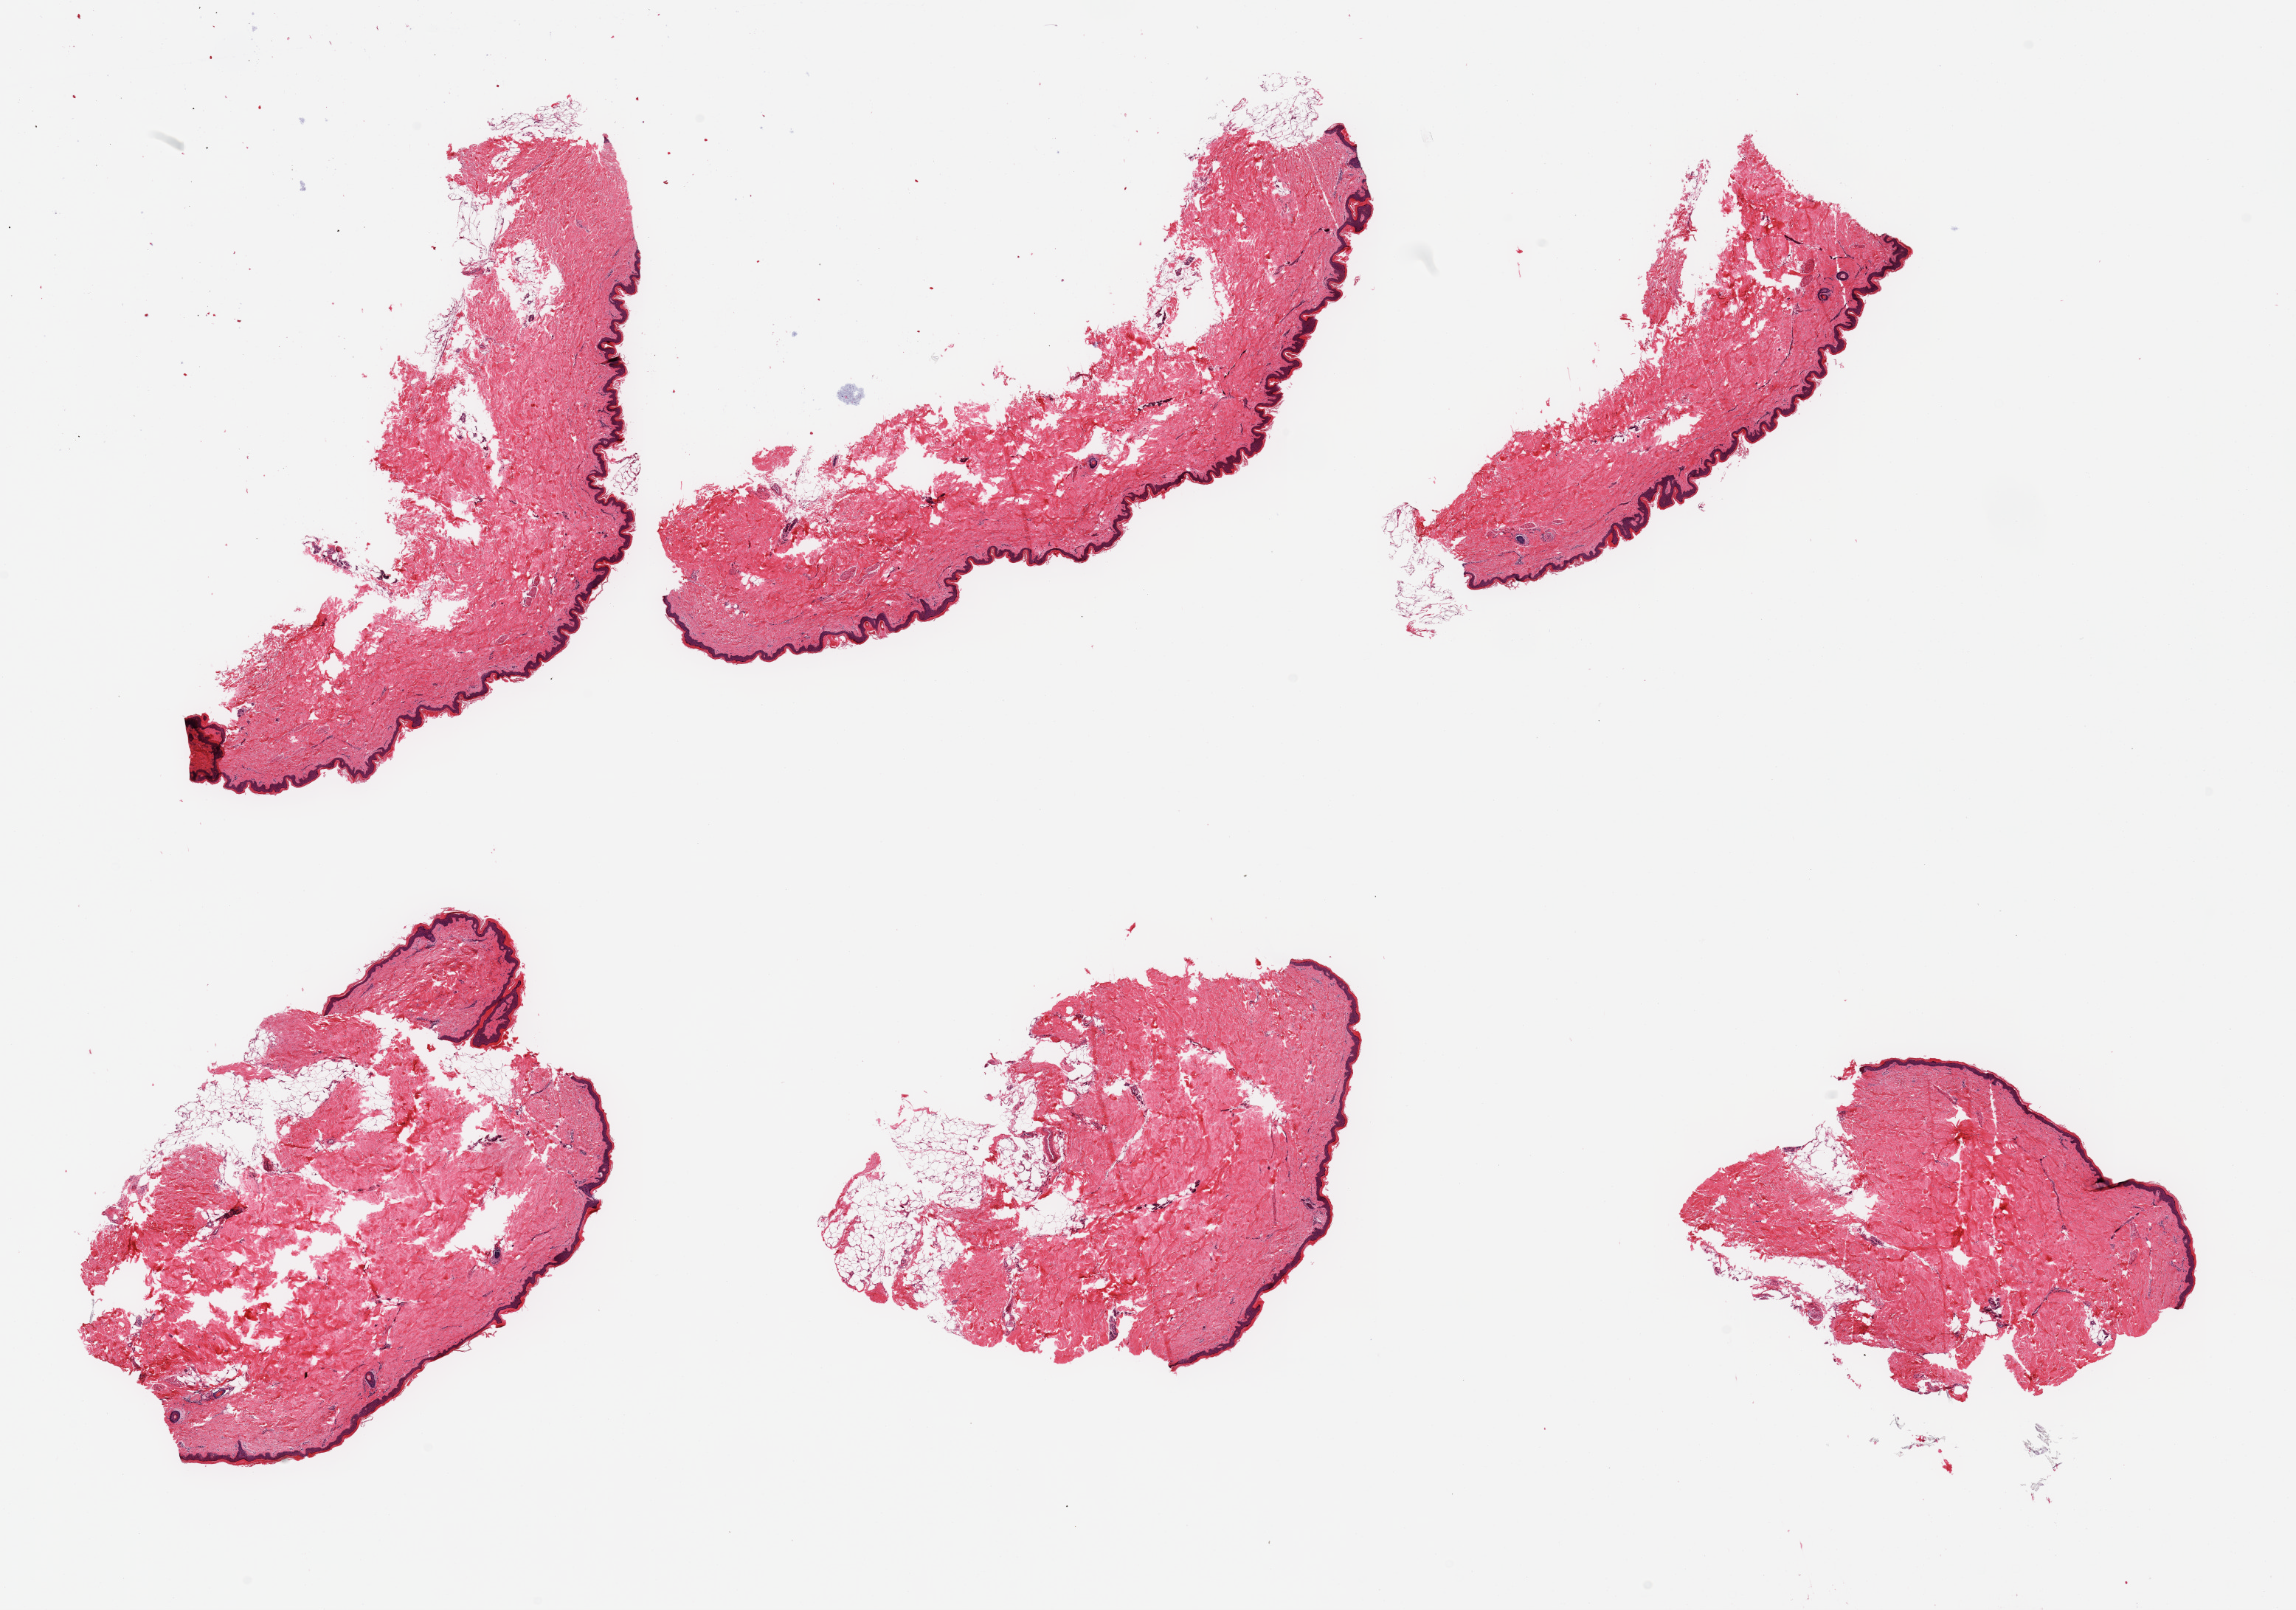
Digitized haematoxylin and eosin-stained section, brightfield — low-resolution overview of the scanned area, about 24.6 x 17.3 mm. PAXgene-fixed paraffin-embedded (PFPE) section. Target tissue: skin of lower leg. Donor tissue sample. Donor sex: female.
Reviewer comment on this tissue sample: 6 pieces; variable amount of residual attached fat, up to 20%, epidermis measures 38 microns.